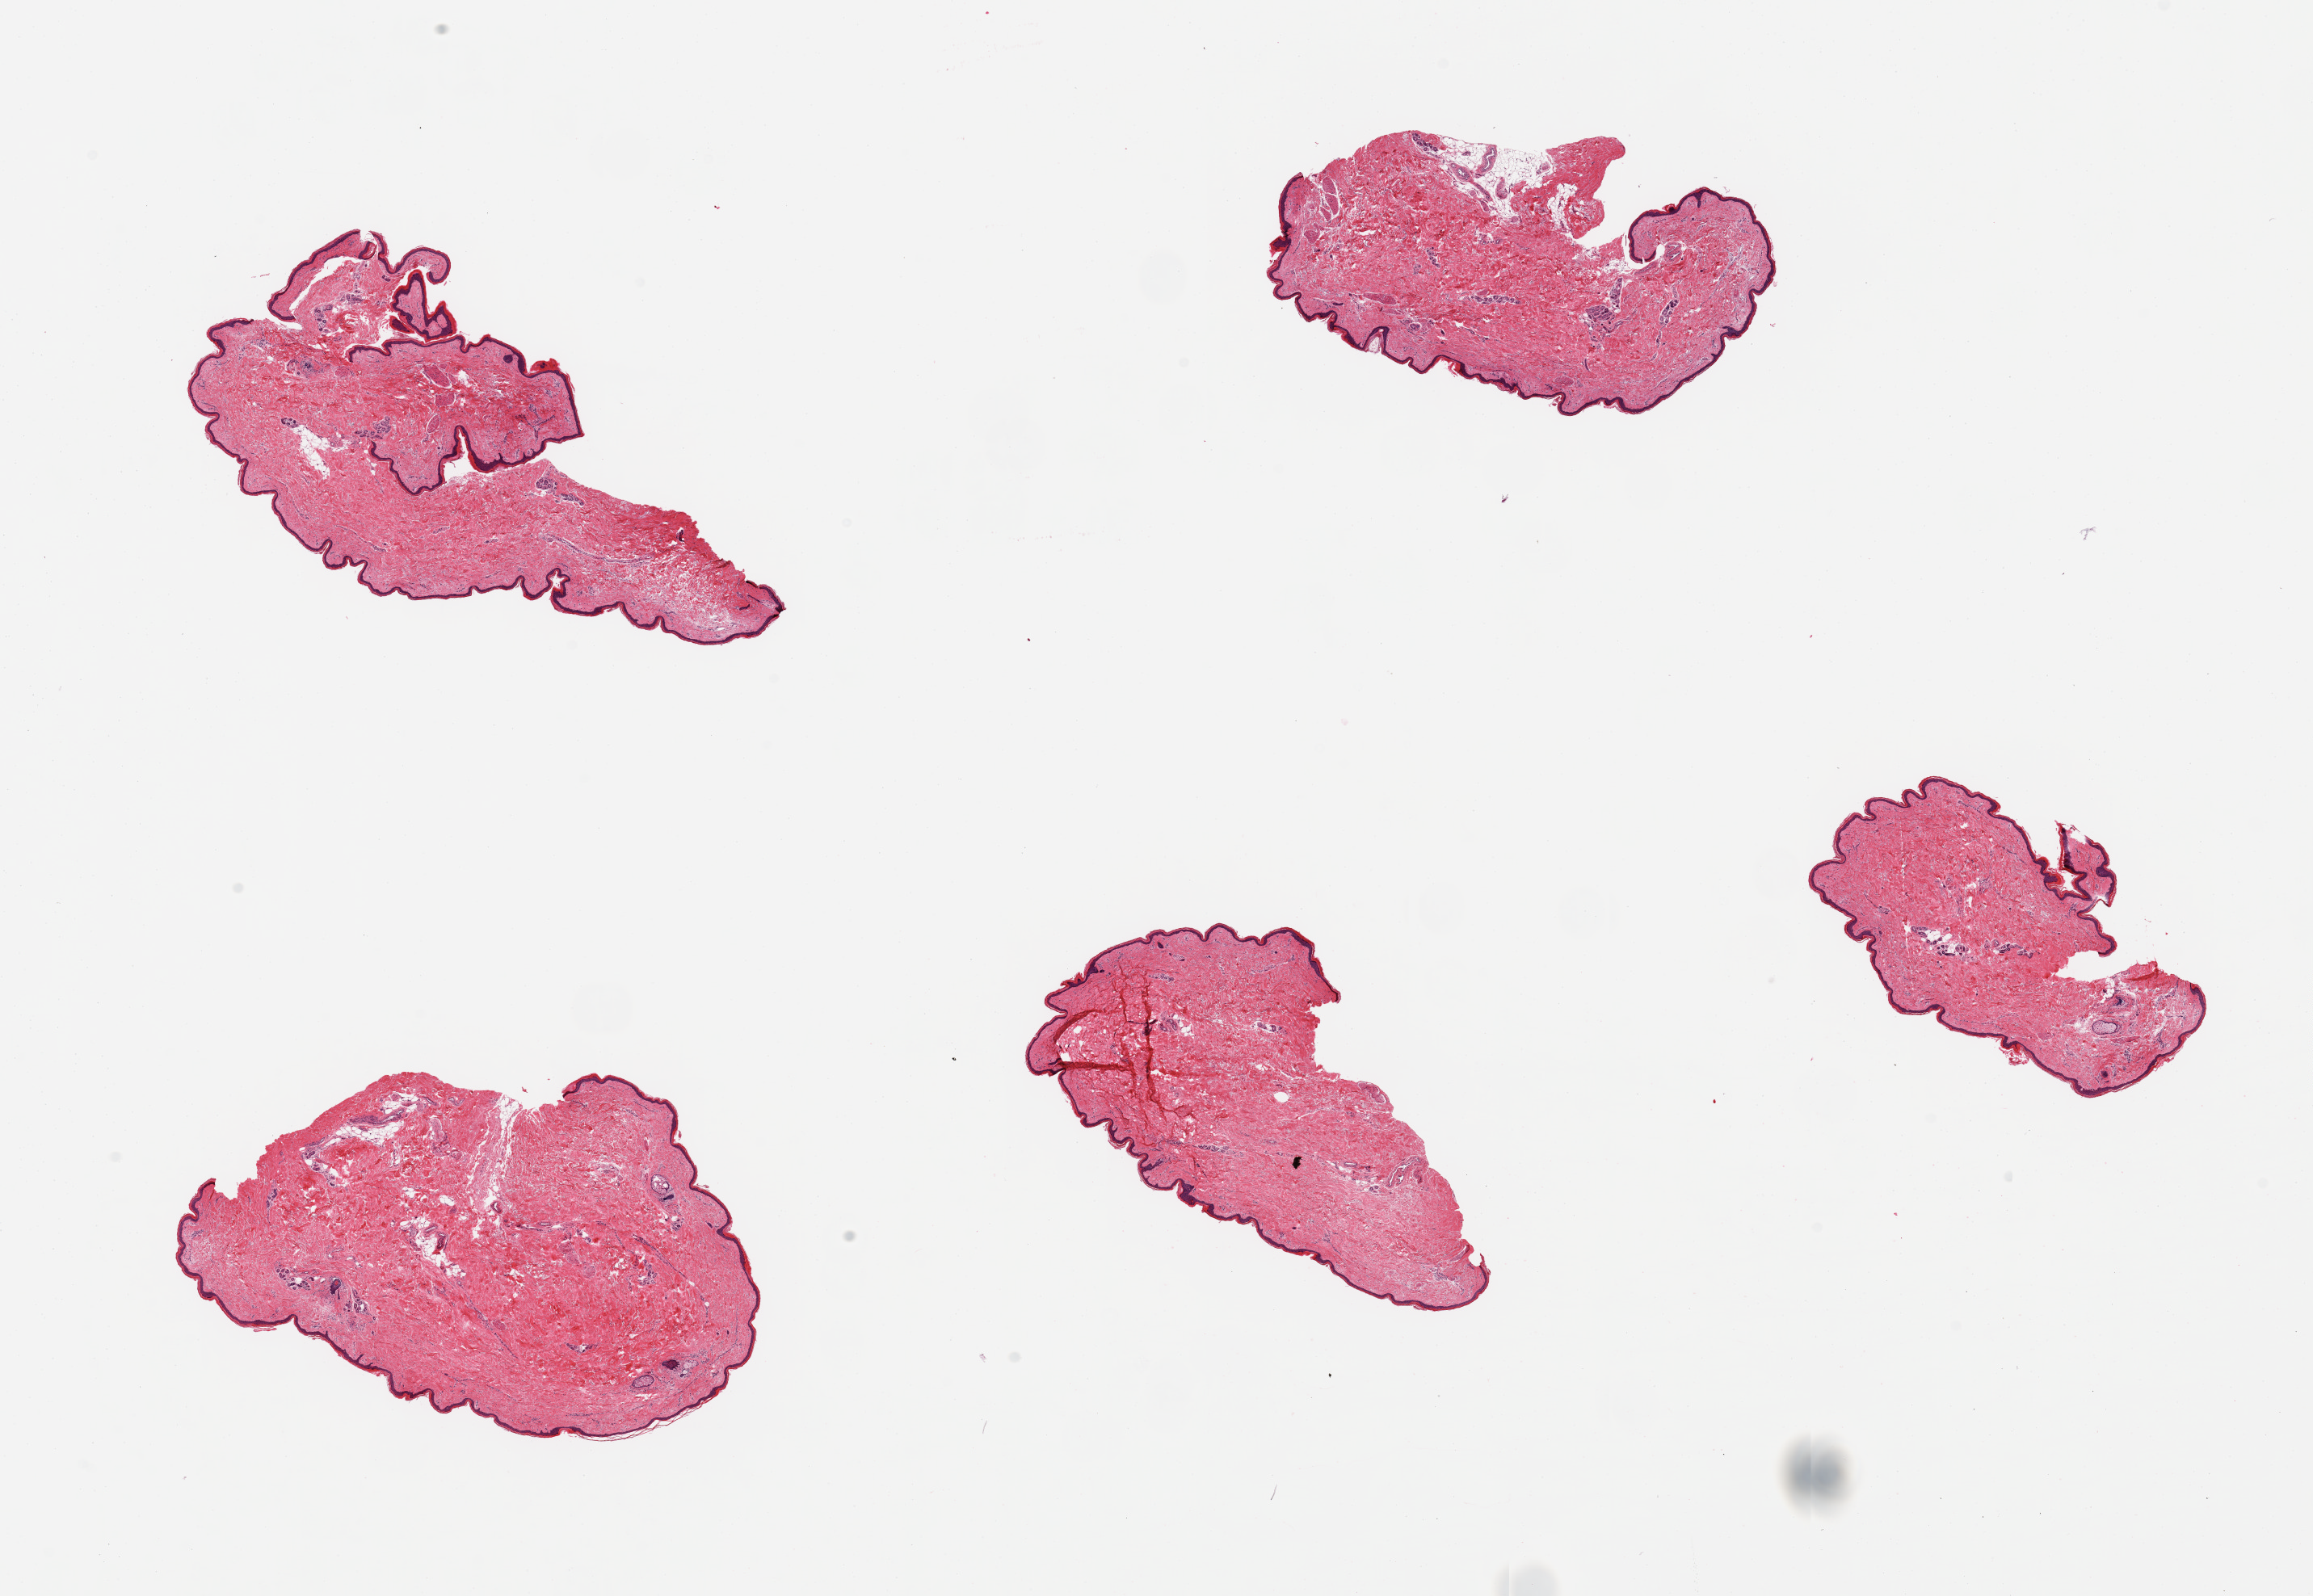
Haematoxylin and eosin whole-slide image, brightfield — whole scanned area (about 22.6 x 15.6 mm, from a 20x scan) shown as a low-resolution overview. PAXgene-fixed paraffin-embedded (PFPE) section. Target tissue: skin of lower leg. Tissue donor sample.
Review note (as recorded): 5 pieces; predominantly well trimmed, epidermis measures 24 to 34 microns thick.